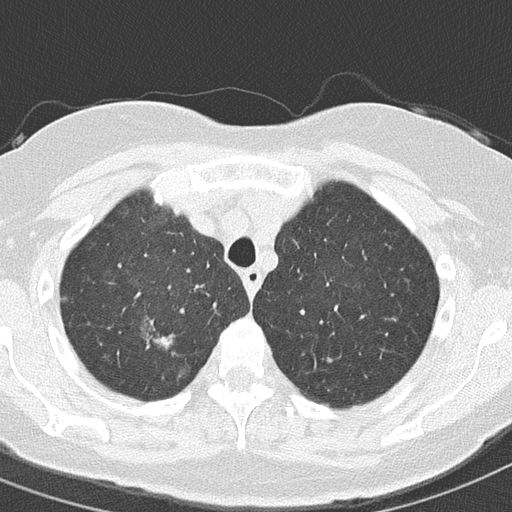
Chest CT (low-dose screening protocol), one axial image, second screening round (one year after baseline), lung window (W 1500 / L -600 HU), 2 mm slice thickness, slice 33 of 157 in the series, 512 × 512 image matrix, field of view 280 × 280 mm. Female participant, aged 61 years at enrolment. Current smoker at enrolment.
Expert reader's lesion annotation, bounding box <144,318,187,359> (left, top, right, bottom; pixels). Reader record for this screening exam (exam-level; its link to the box is not recorded): non-calcified nodule or mass ≥4 mm, right upper lobe, 15 × 10 mm, spiculated (stellate) margins, ground glass attenuation, pre-existing on the prior screen: yes; interval growth: yes. Official screen result: positive, other. Participant outcome: lung cancer diagnosed 91 days after this screen — adenocarcinoma, NOS, right upper lobe, moderately differentiated (G2), stage IA (AJCC 6th edition), 20 mm at pathology.